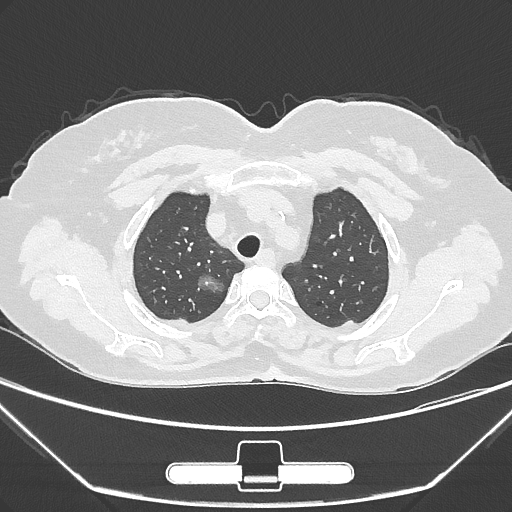
Chest CT, one axial slice; position 230 of 275 along the scan axis; reconstruction kernel IMR1,SharpPlus; lung window (W 1500 / L -600 HU); 1 mm slice thickness; 512 × 512 image matrix. Patient: female, 63 years. From the clinical record (not read from this slice): clinical TNM (as recorded): T1a N0 M0; histopathological grade: G1.
Annotated regions visible in this slice (rectangle marked by the reading radiologist):
- lung tumour (recorded histology: adenocarcinoma): bounding box <189,264,234,304> (left, top, right, bottom; pixels)